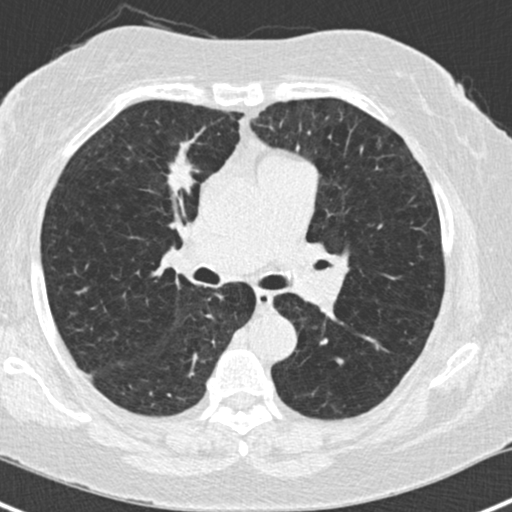
Low-dose screening chest CT, one axial slice. Position 89 of 168 along the scan axis. Reconstruction kernel B30f. 120 kVp. Lung window (W 1500 / L -600 HU). 512 × 512 image matrix, field of view 303 × 303 mm.
Structures marked on this image (expert manual segmentation):
- lesion 1 (tumor, upper lobe of right lung): bounding box (x1, y1, x2, y2) in pixels: (168, 152, 195, 197)